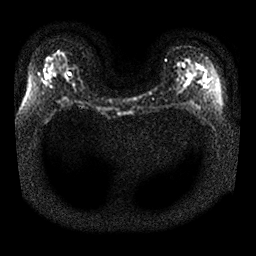
Breast MRI, one axial slice. Slice 17 of 25 in the series (ordered by position). Diffusion-weighted series; image 2 of 4 stored at this slice position (different b-values; order by instance number). 1.5 T. 4 mm slice thickness. 256 × 256 image matrix. Female patient.
Outlined on this slice (manually delineated by an expert):
- tumour on diffusion-weighted imaging: bounding box <48,70,54,78> (left, top, right, bottom; pixels)